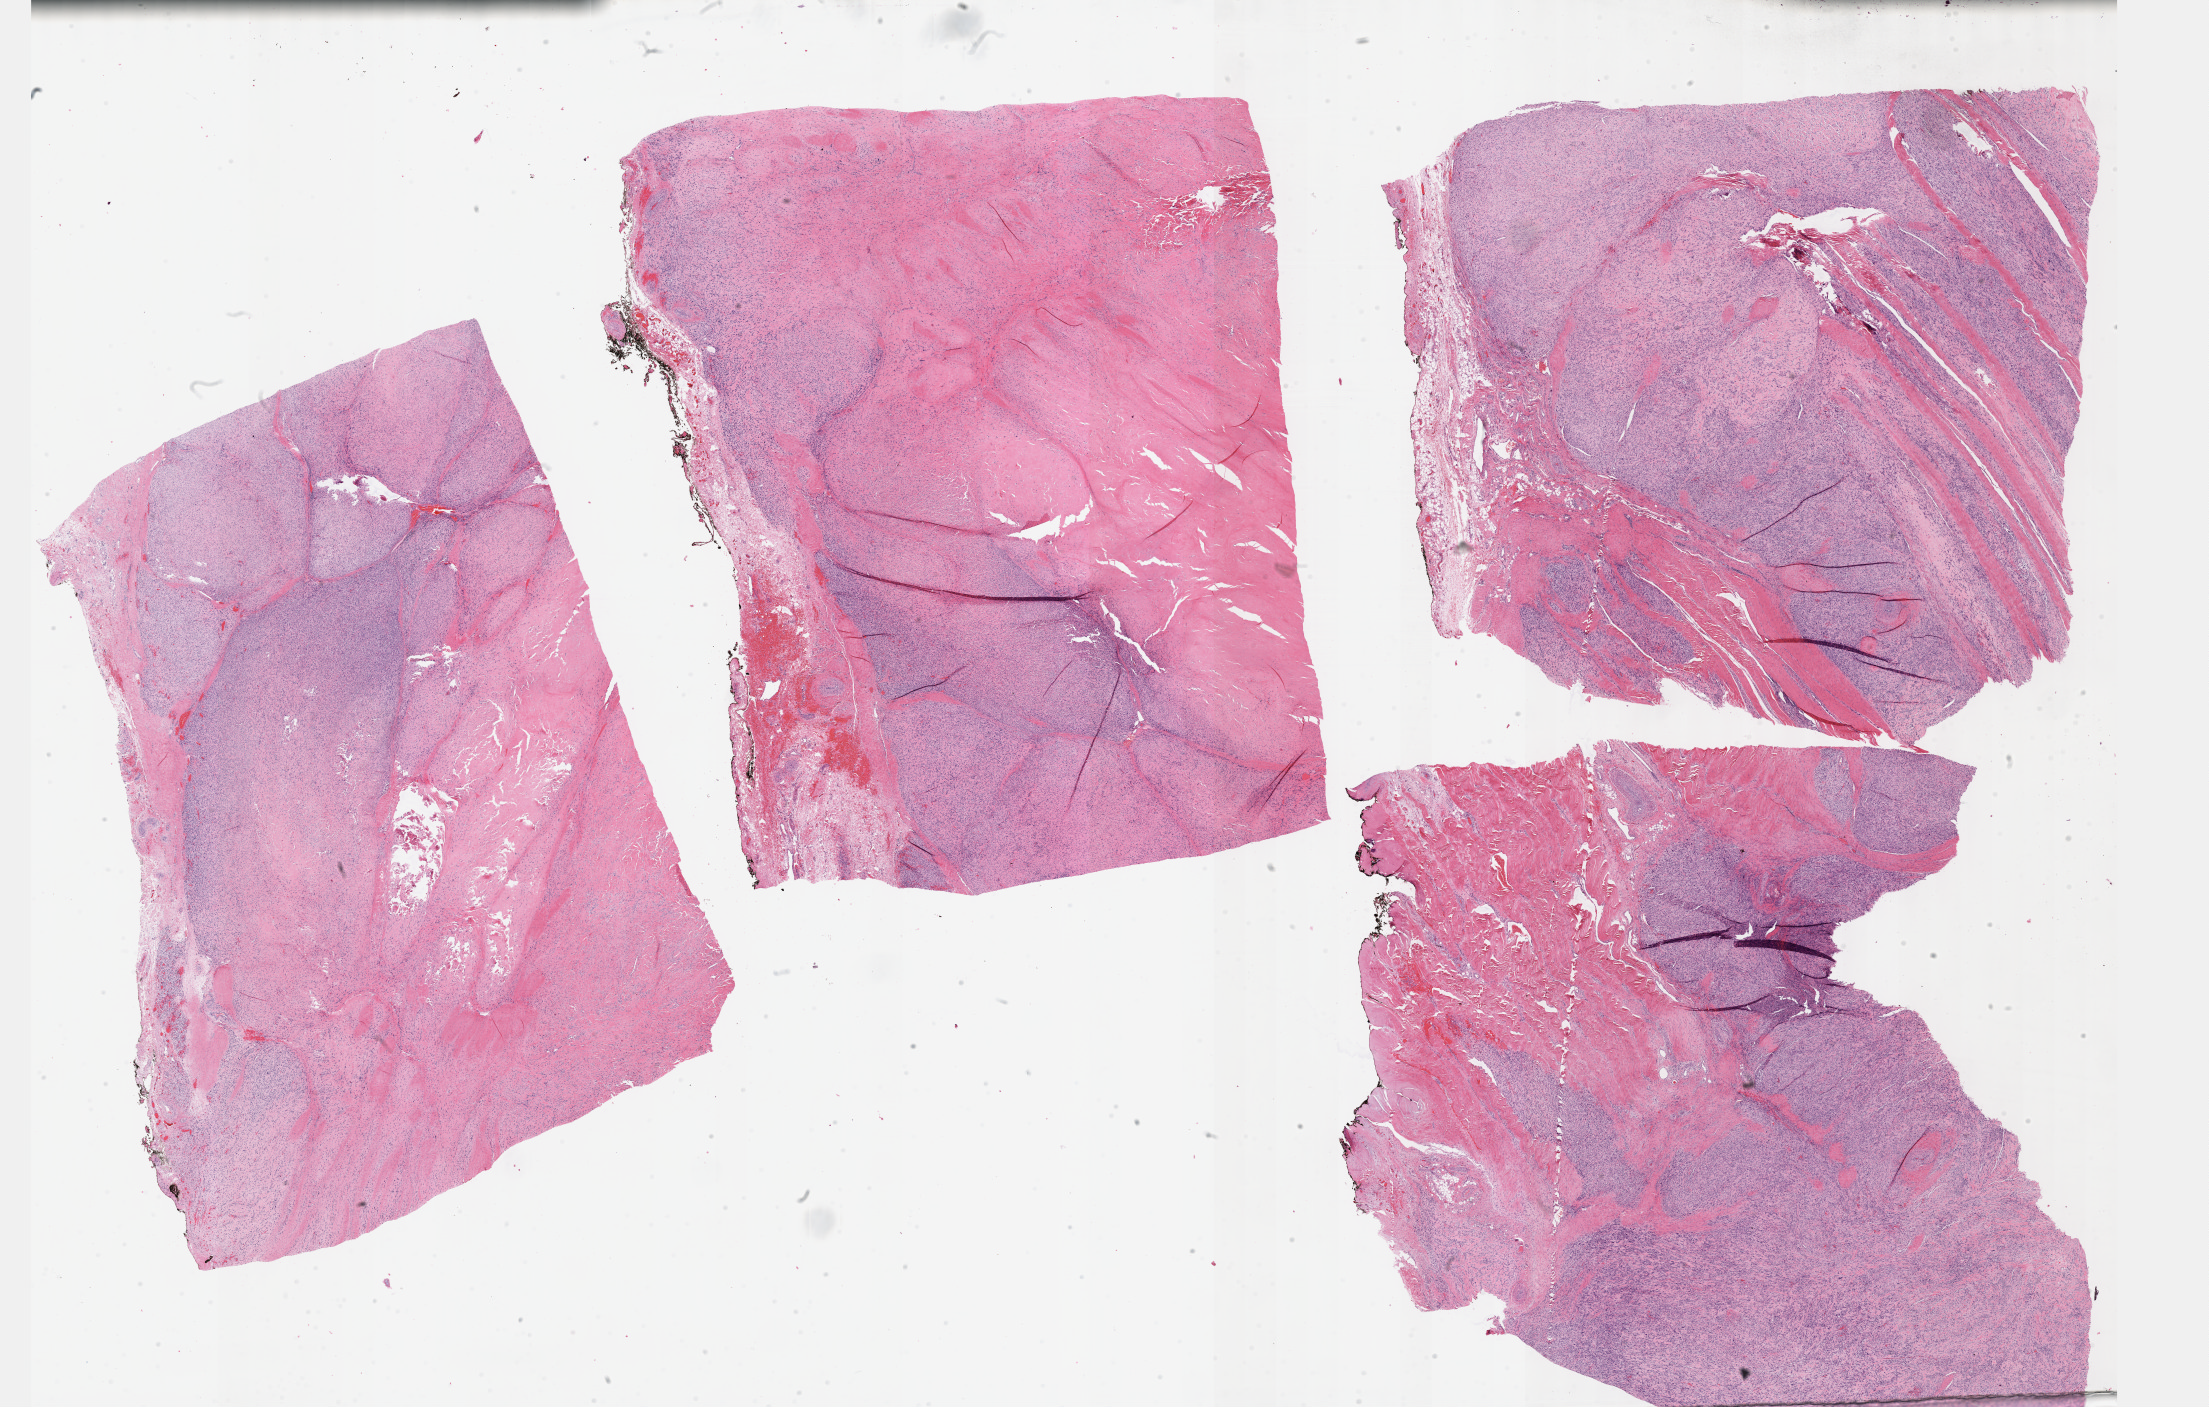
Whole-slide histology image, H&E-stained — a low-resolution overview of the entire scanned area, about 35.7 x 22.7 mm. Formalin-fixed paraffin-embedded (FFPE) diagnostic section. Sample: primary tumour, connective, subcutaneous and other soft tissues. Patient: male, age at initial diagnosis 74 years.
Pathologic diagnosis: Leiomyosarcoma, NOS (connective, subcutaneous and other soft tissues of lower limb and hip).